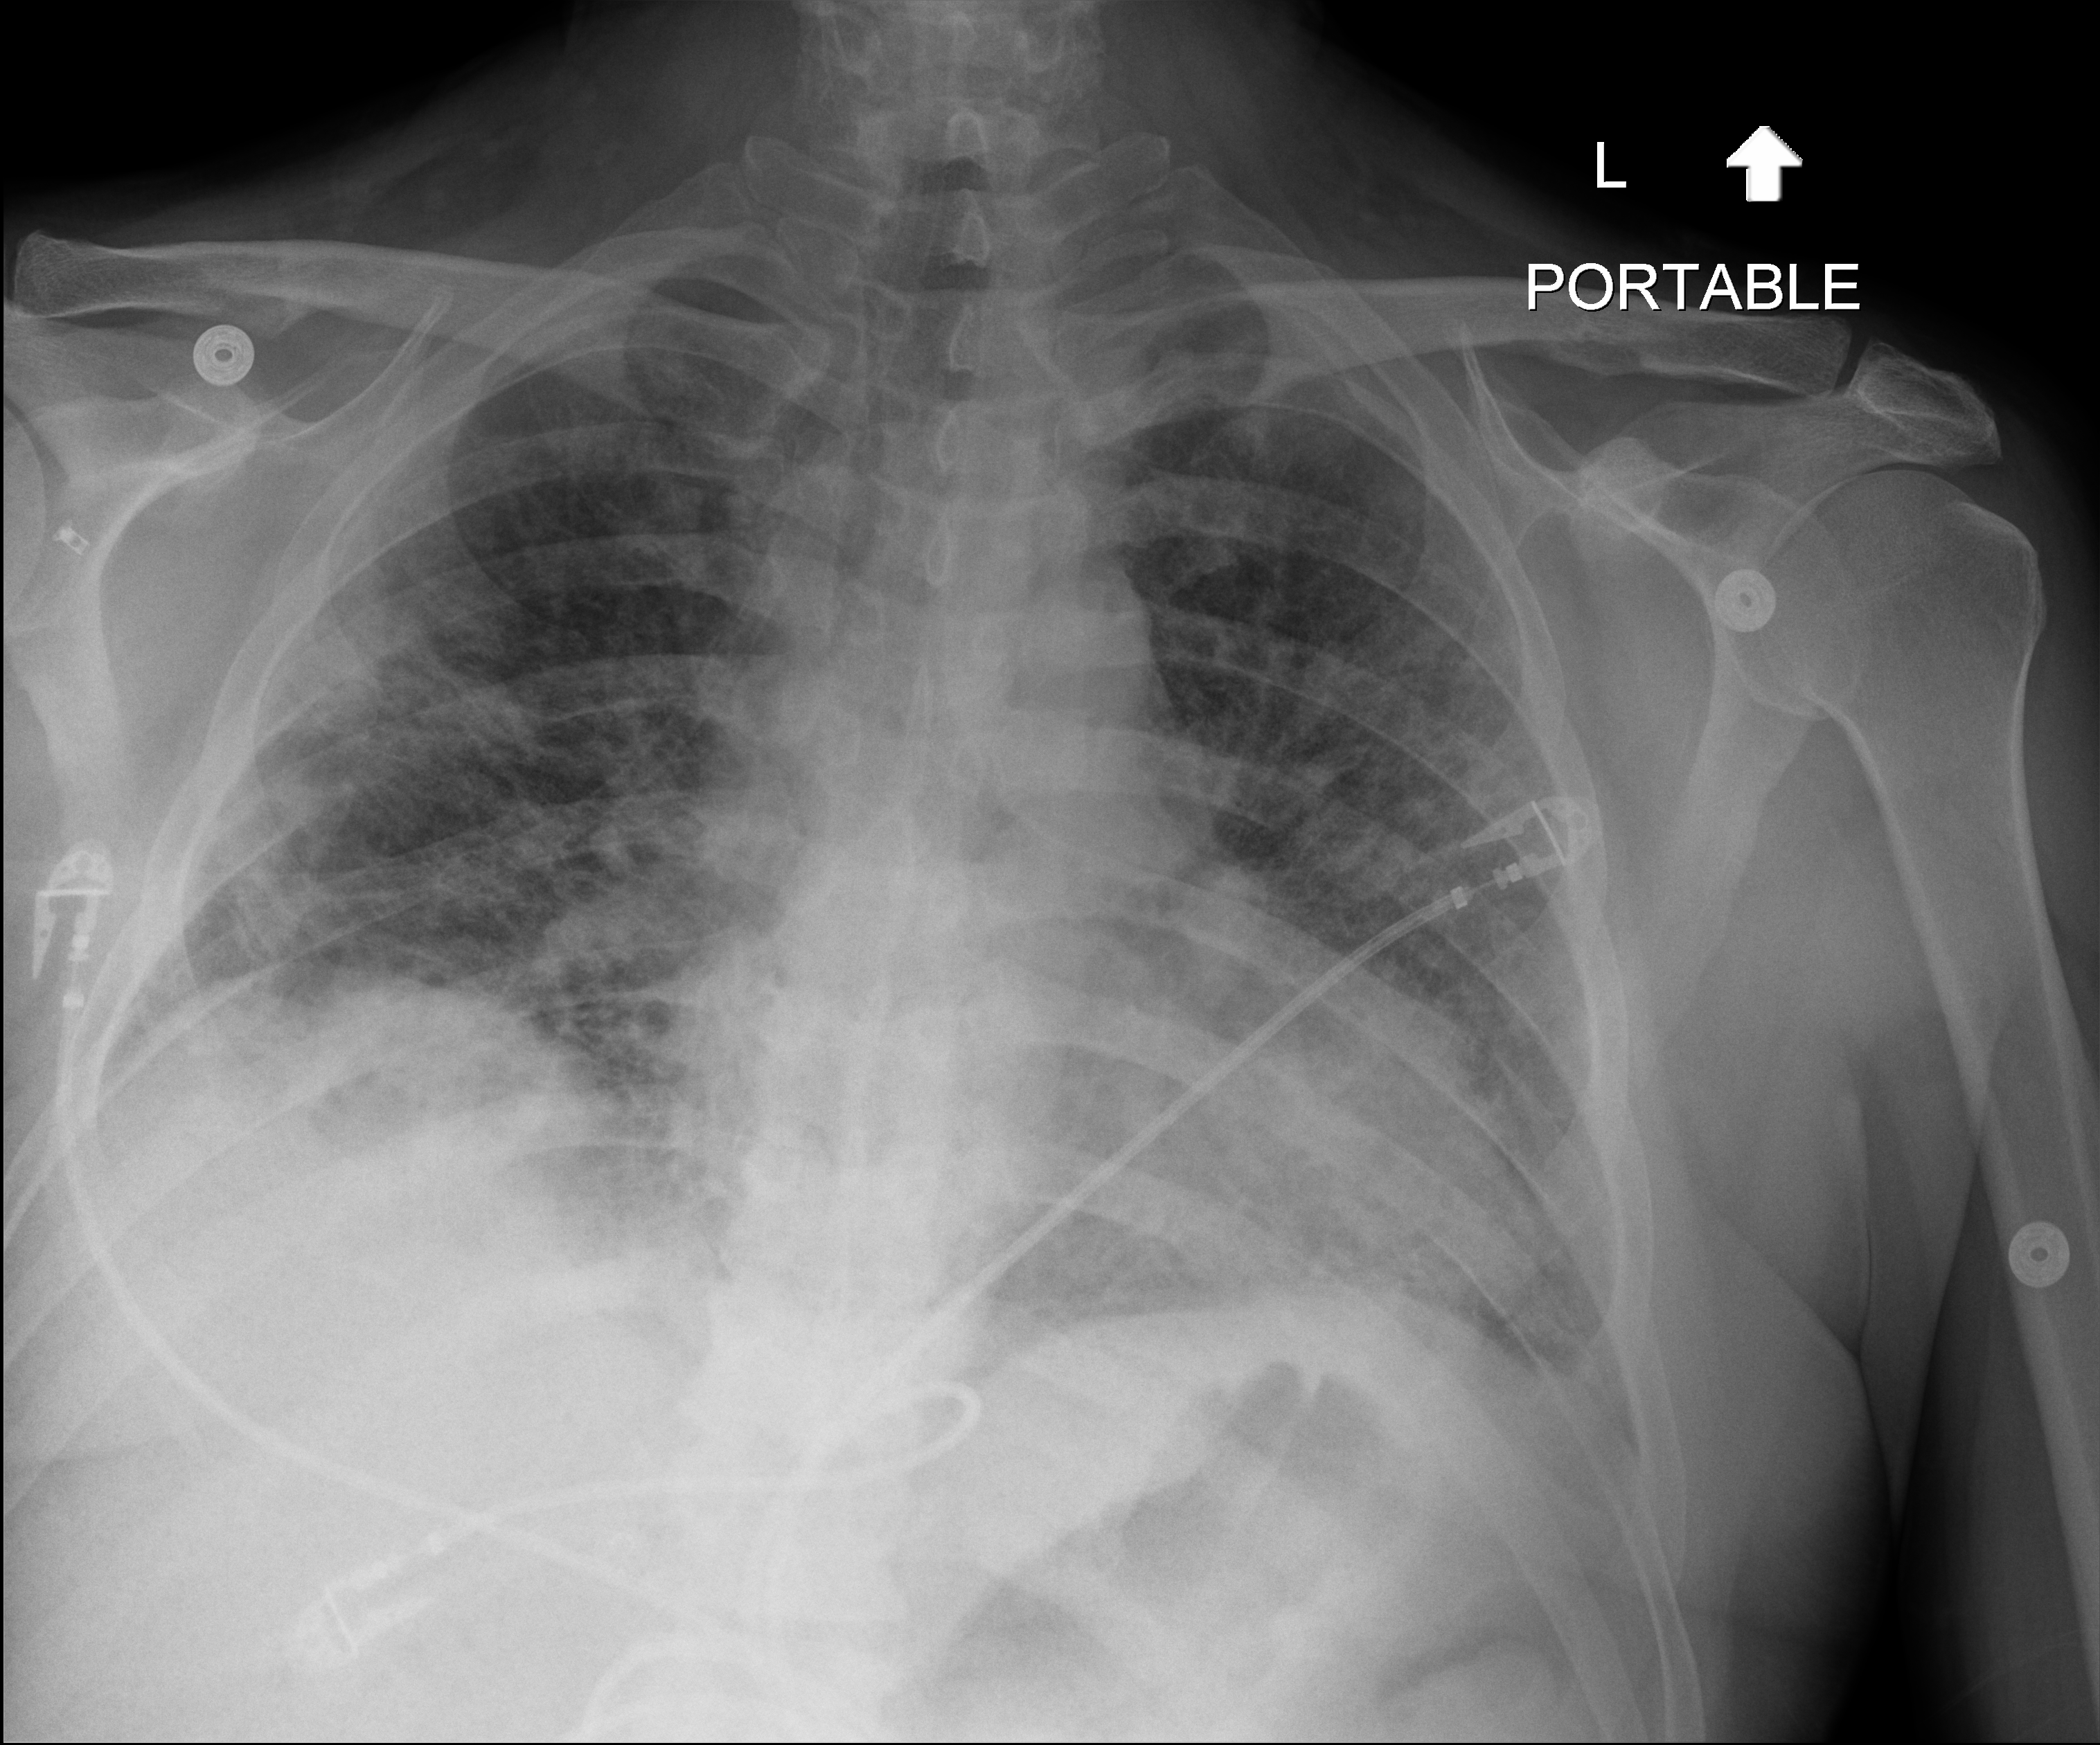
Chest X-ray (portable); anteroposterior (AP) projection. Male patient hospitalised with COVID-19, age 18–59 years.
From the hospital-stay record, not from the radiograph (when in the stay this image was taken is not recorded):
- diabetes (admission record): no
- mechanically ventilated during this hospital stay: yes